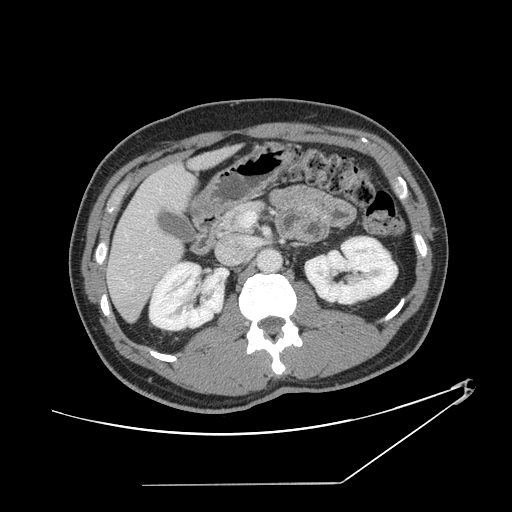
Contrast-enhanced abdominal CT, one axial slice. Position 68 of 152 along the scan axis. Reconstruction kernel STANDARD. Intravenous contrast given. Soft-tissue window (W 400 / L 40 HU). 2.5 mm slice thickness. 512 × 512 image matrix. Male patient, age 45 years. Case-level facts recorded for this patient, not image findings: diagnosis: colorectal cancer liver metastases, imaged before liver resection; multiple liver metastases: no; largest metastasis: 1 cm; disease in both lobes: no.
Annotated regions visible in this slice (outlined manually by an expert reader):
- hepatic veins: bounding box [x1, y1, x2, y2] px = [124, 188, 162, 259]
- liver: [108, 148, 233, 320]
- planned liver remnant (the part of the liver to remain after resection): [108, 166, 195, 320]
- portal vein (with intrahepatic branches): [241, 211, 256, 227]